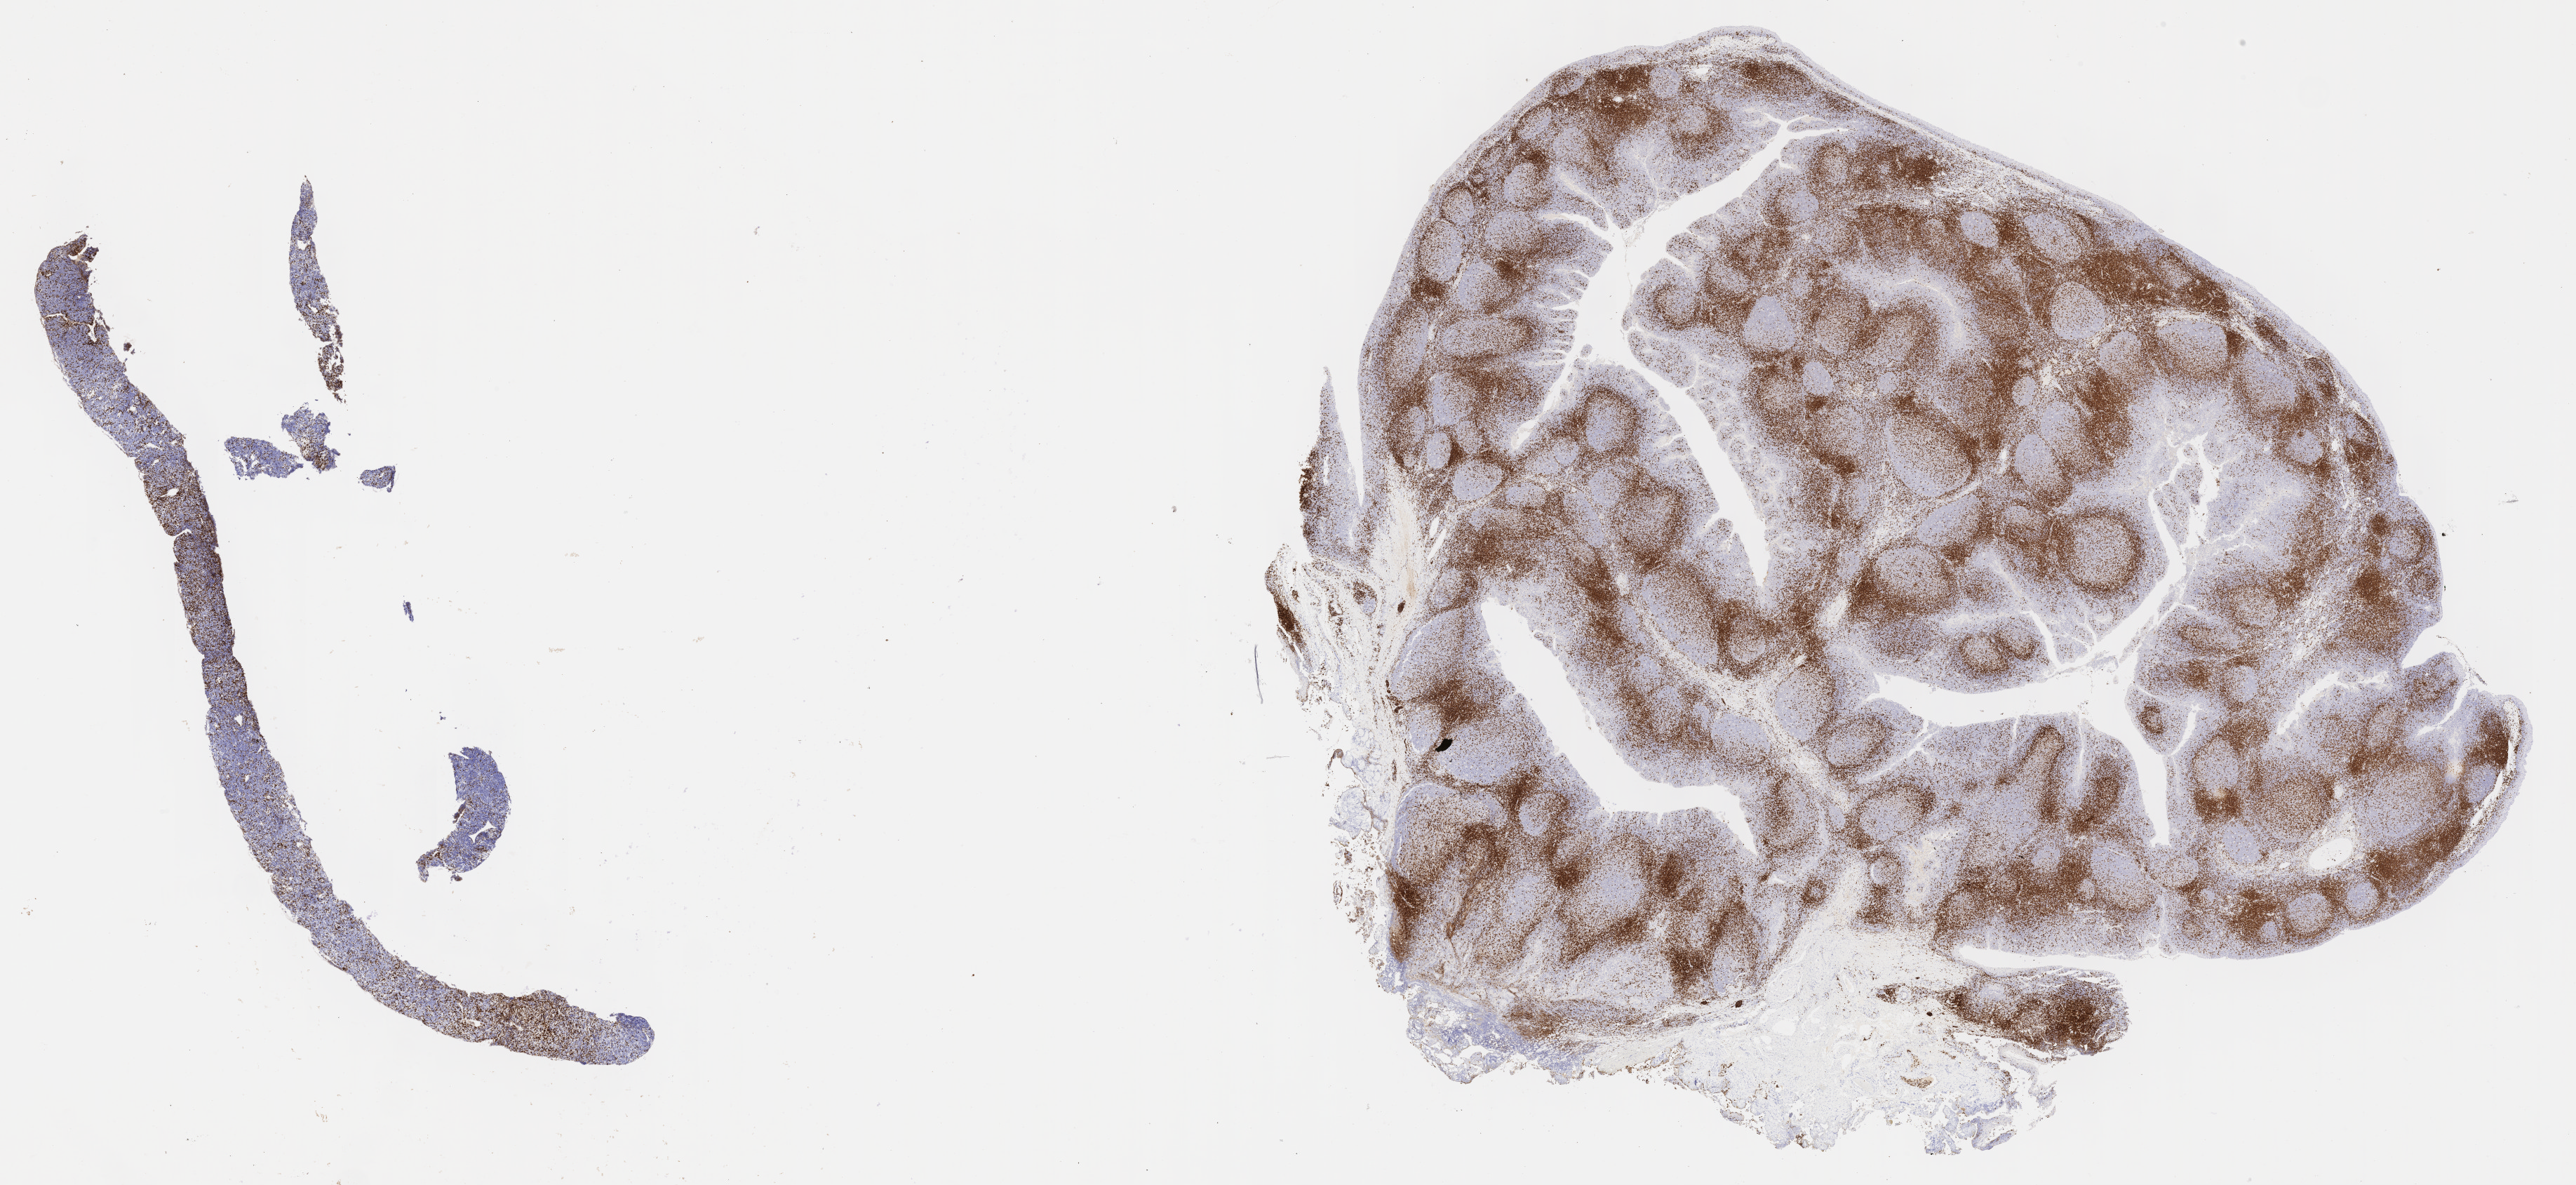
Whole-slide image, immunohistochemical stain for CD3, shown as a low-resolution overview of the whole scanned area (about 29.7 x 13.7 mm), specimen: tumor tissue, site: ovary. Female patient; age at initial diagnosis 9 years.
Diagnosis: Burkitt lymphoma, NOS.